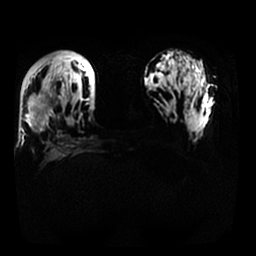
Breast MRI, one axial slice. Position 12 of 25 along the scan axis. Diffusion-weighted series; image 2 of 4 stored at this slice position (different b-values; order by instance number). 1.5 T. 256 × 256 image matrix, field of view 340 × 340 mm. Female patient.
Structures marked on this image (outlined manually by an expert reader):
- tumour on diffusion-weighted imaging: bounding box (x1, y1, x2, y2) in pixels: (31, 93, 54, 116)